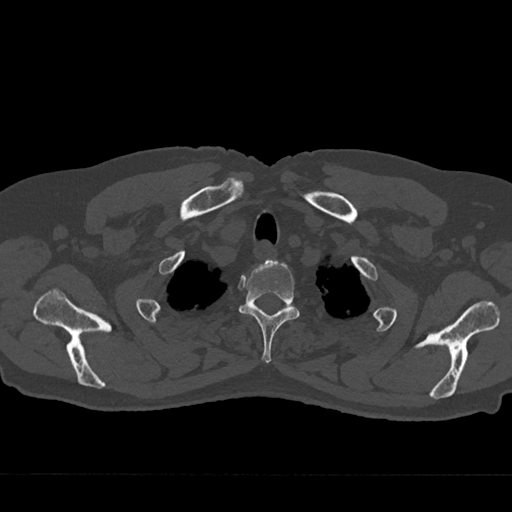
CT including the spine, one axial slice. Slice 612 of 797 in the series (ordered by position). Reconstruction kernel Br40s/3. 120 kVp. Bone window (W 1800 / L 400 HU). 0.5 mm slice thickness. 512 × 512 image matrix, field of view 377 × 377 mm. Male patient, age 75 years. From the clinical record (not read from this slice): primary cancer: renal.
Outlined on this slice (semi-automatically segmented with operator editing):
- T2 vertebra: bounding box <238,259,300,363> (left, top, right, bottom; pixels)